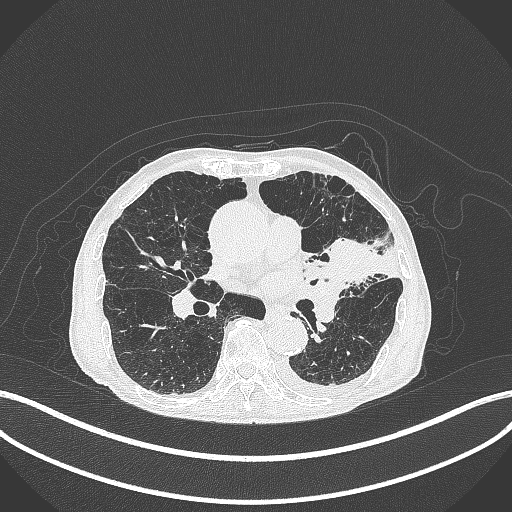
Chest CT, one axial slice; position 198 of 385 along the scan axis; 120 kVp; lung window (W 1500 / L -600 HU); 1 mm slice thickness; 512 × 512 image matrix, field of view 400 × 400 mm. Male patient, age 90 years or older. Case-level facts recorded for this patient, not image findings: clinical TNM (as recorded): T2b N1 M0.
Structures marked on this image (rectangle marked by the reading radiologist):
- lung tumour (recorded histology: squamous cell carcinoma): box from (x=323, y=230) to (x=382, y=288) px